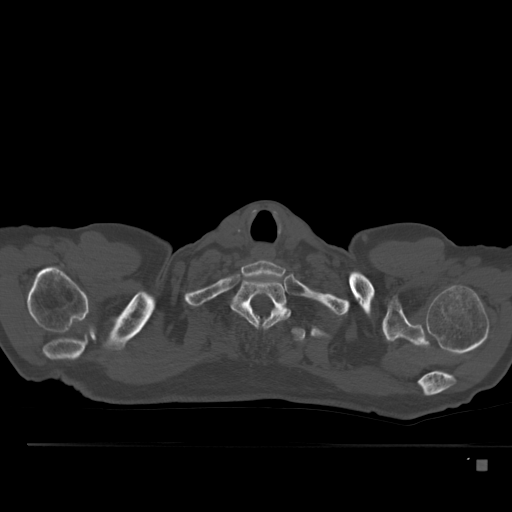
CT including the spine, one axial slice. Position 425 of 517 along the scan axis. Reconstruction kernel Br40s. 120 kVp. Bone window (W 1800 / L 400 HU). 512 × 512 image matrix, field of view 408 × 408 mm. Male patient, age 70 years. Case-level facts recorded for this patient, not image findings: primary cancer: renal.
Annotated regions visible in this slice (semi-automatic segmentation, software-assisted and operator-edited):
- T1 vertebra: bounding box [x1, y1, x2, y2] px = [232, 278, 291, 328]
- T2 vertebra: [249, 305, 306, 342]